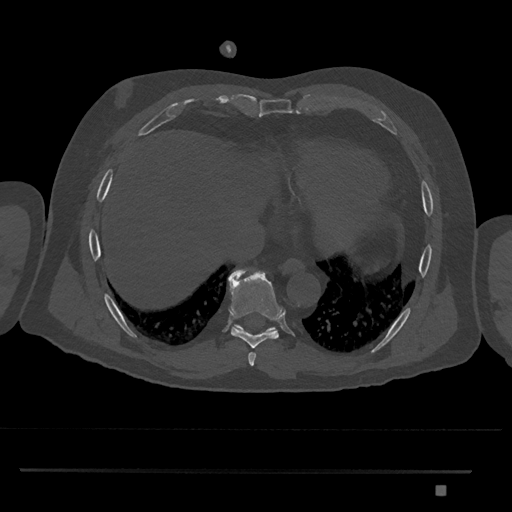
CT including the spine, one axial slice. Slice 1099 of 1134 in the series (ordered by position). Reconstruction kernel Br40s/3. 120 kVp. Bone window (W 1800 / L 400 HU). 0.5 mm slice thickness. 512 × 512 image matrix. Male patient, age 65 years. From the clinical record (not read from this slice): primary cancer: prostate.
Outlined on this slice (semi-automatically segmented with operator editing):
- T8 vertebra: bounding box [x1, y1, x2, y2] px = [228, 269, 284, 348]
- T9 vertebra: [234, 324, 276, 332]